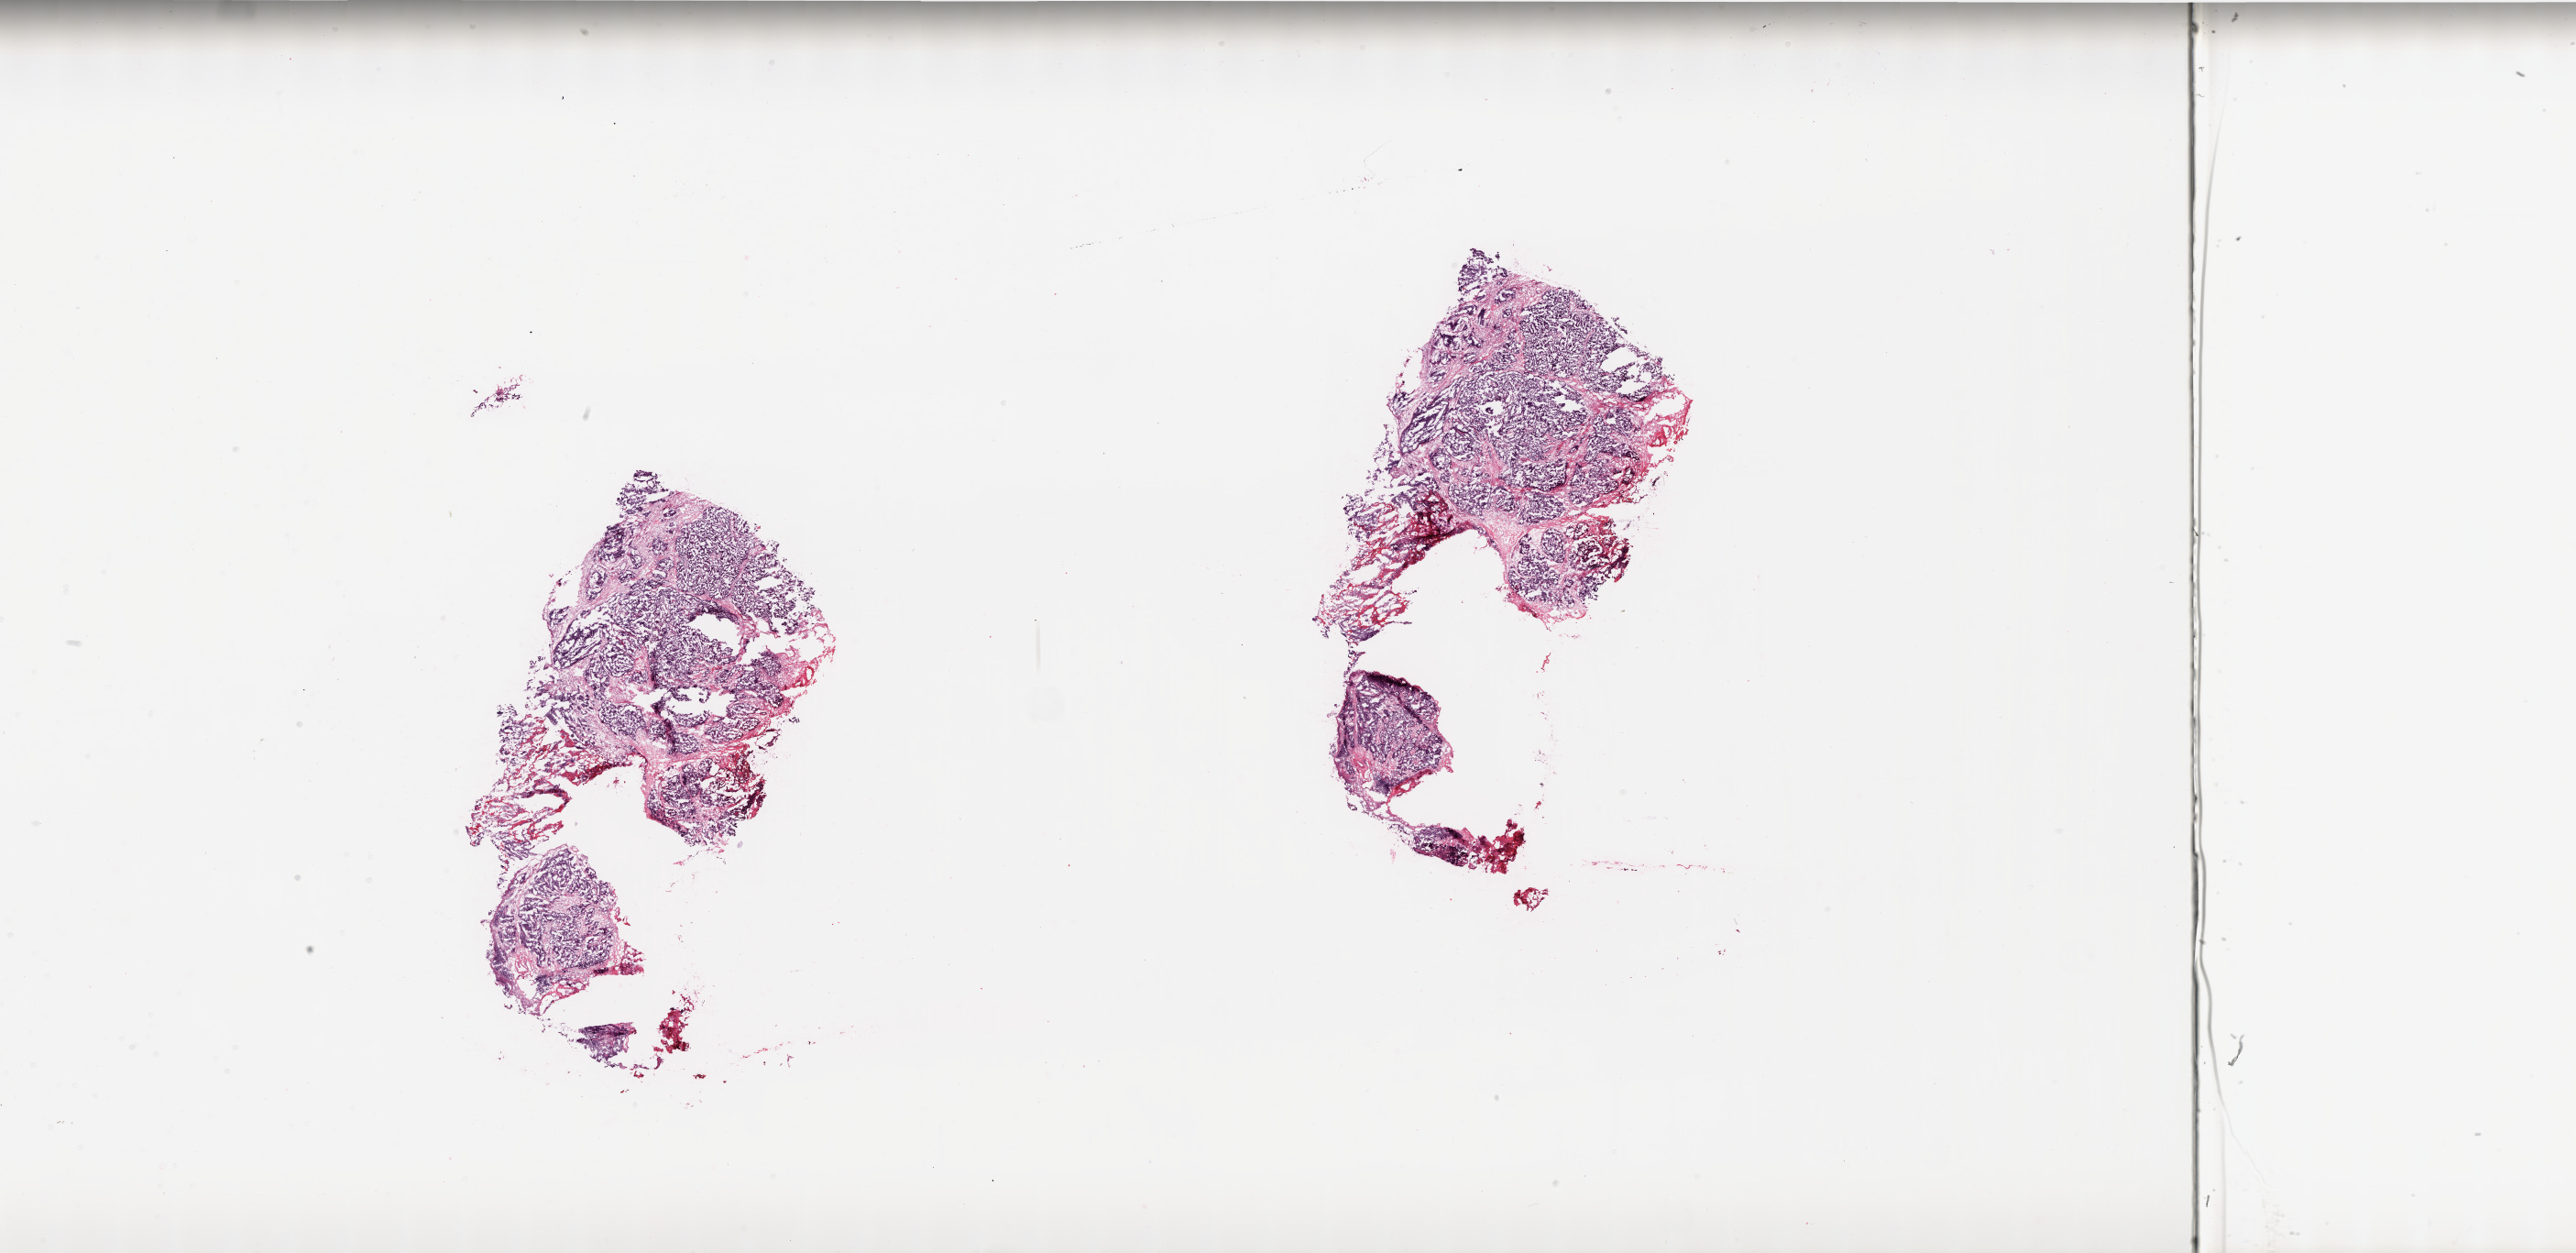
Digitized H&E tissue section (whole slide), low-resolution overview of the scanned area, about 44.9 x 21.8 mm, frozen section from the top of the tissue portion, primary tumour sample from the ovary. Patient: female, age at initial diagnosis 78 years. Histologic grade: G3 (poorly differentiated). Slide review estimates, as recorded: tumour cells 78%, tumour nuclei 90%, normal cells 0%, stromal cells 20%, necrosis 2%.
* FIGO stage: IIIC
* histologic diagnosis: Serous cystadenocarcinoma, NOS